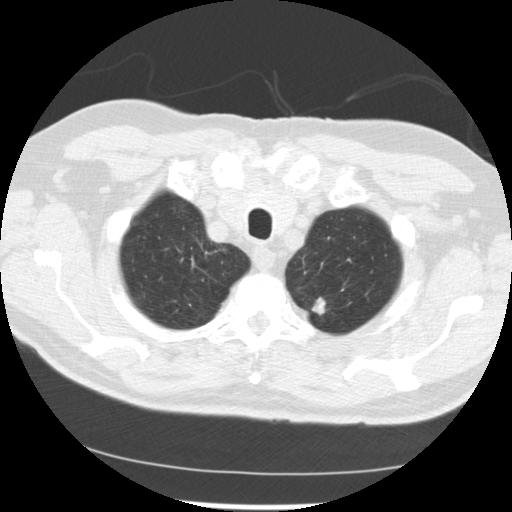
Low-dose screening chest CT, one axial slice. Slice 218 of 249 in the series (ordered by position). Lung window (W 1500 / L -600 HU). 2.5 mm slice thickness. 512 × 512 image matrix, field of view 341 × 341 mm.
Annotated regions visible in this slice (expert manual segmentation):
- lesion 2 (tumor, upper lobe of left lung): box from (x=312, y=298) to (x=326, y=314) px